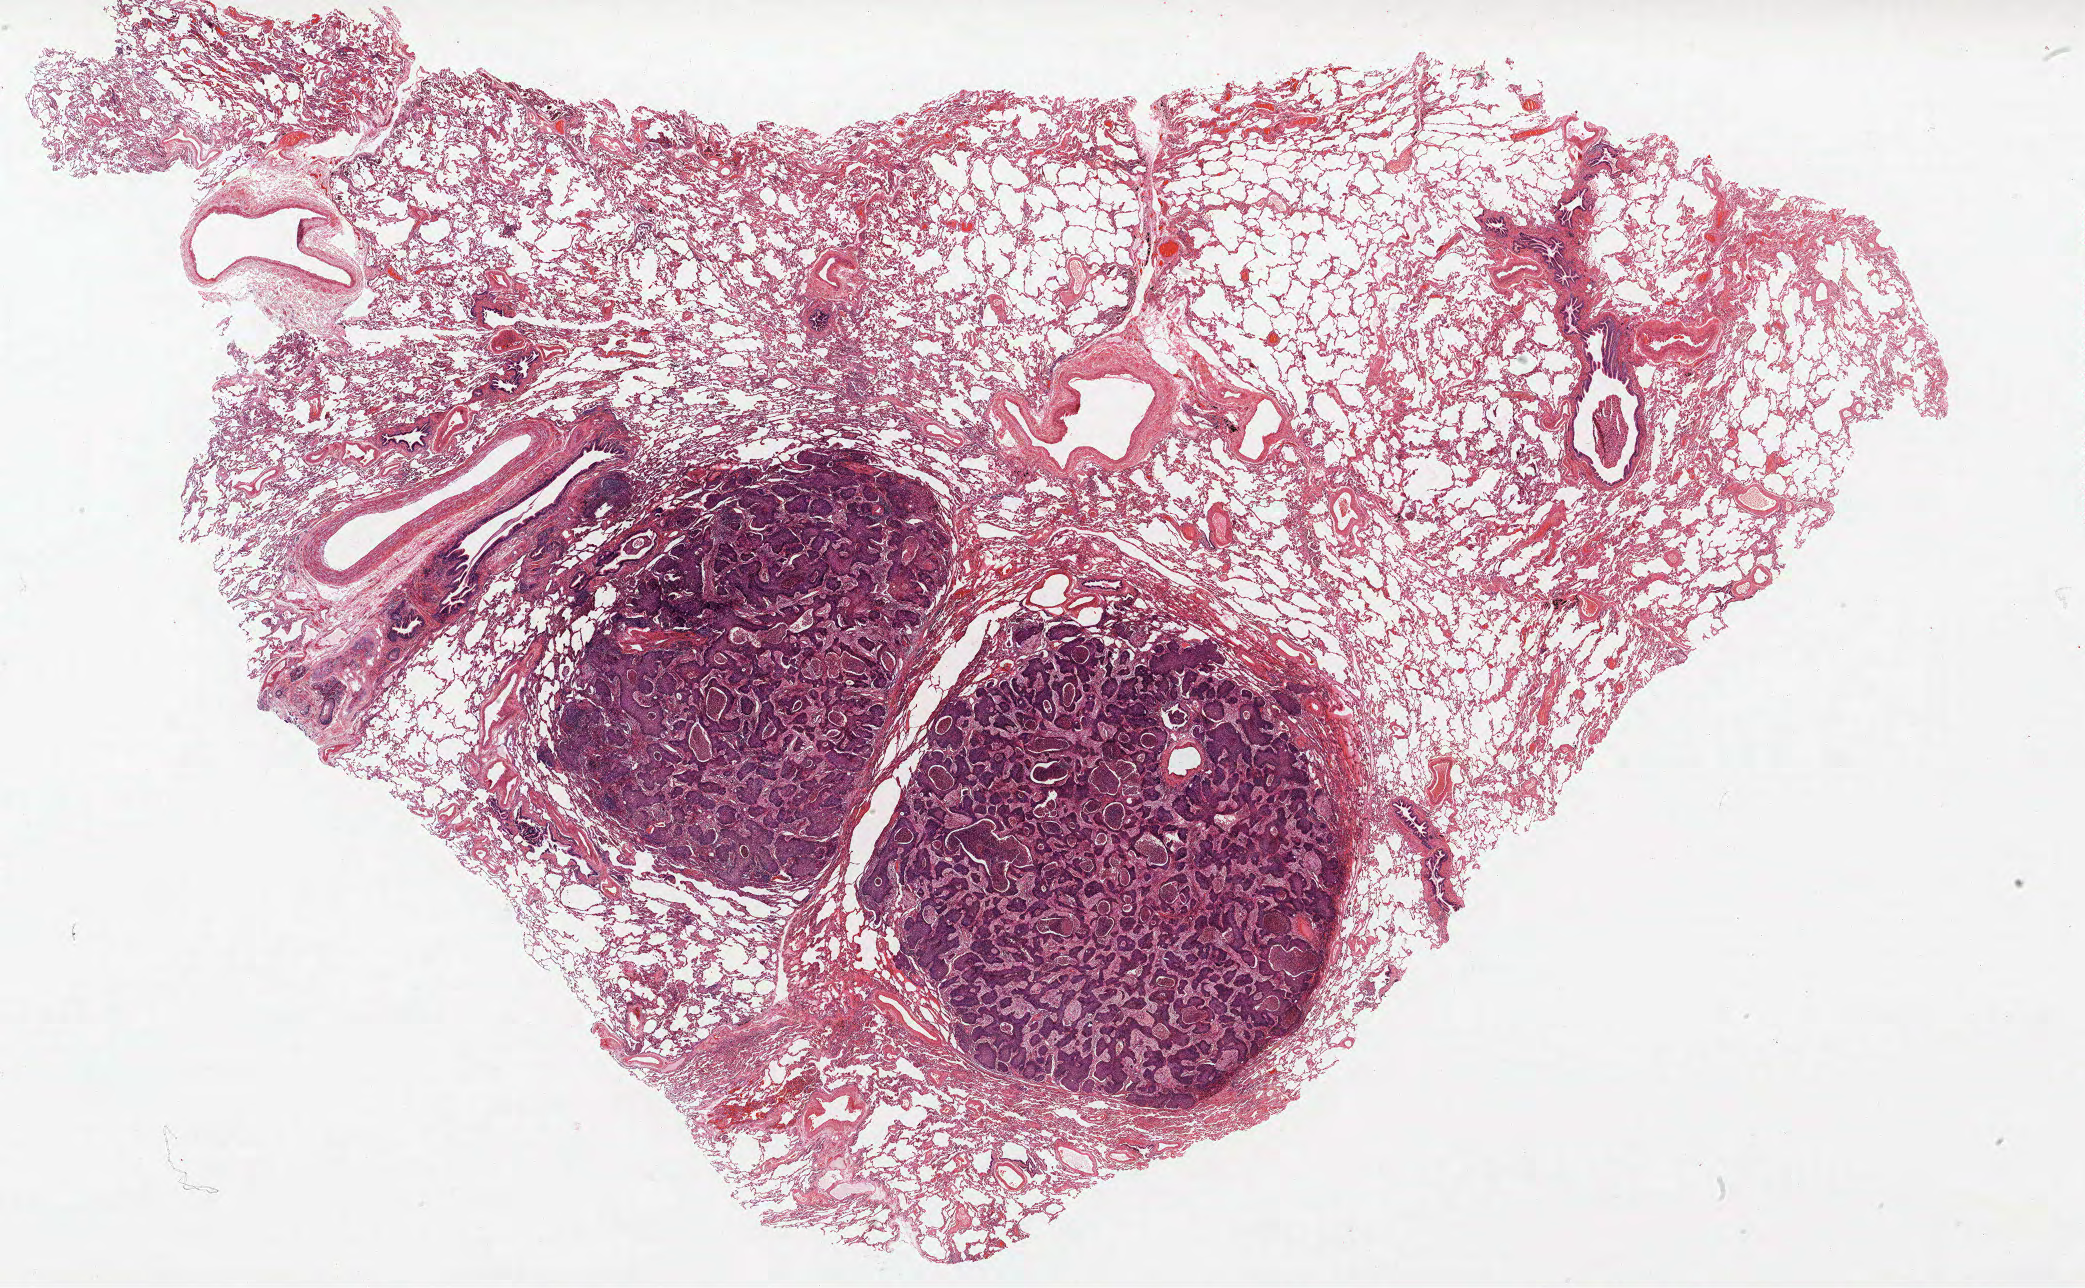
H&E whole-slide image, low-resolution overview of the scanned area, about 33.4 x 20.6 mm (slide scanned at 40x), FFPE section, lung tissue. Male patient, aged 69 at enrolment. Grade: poorly differentiated (G3).
Primary tumour location (clinical record): right upper lobe. Participant's lung-cancer diagnosis: Squamous cell carcinoma, large cell, nonkeratinizing, NOS (ICD-O-3 8072/3). Tumour size (pathology): 7 mm. Stage (AJCC 6th edition): IA.